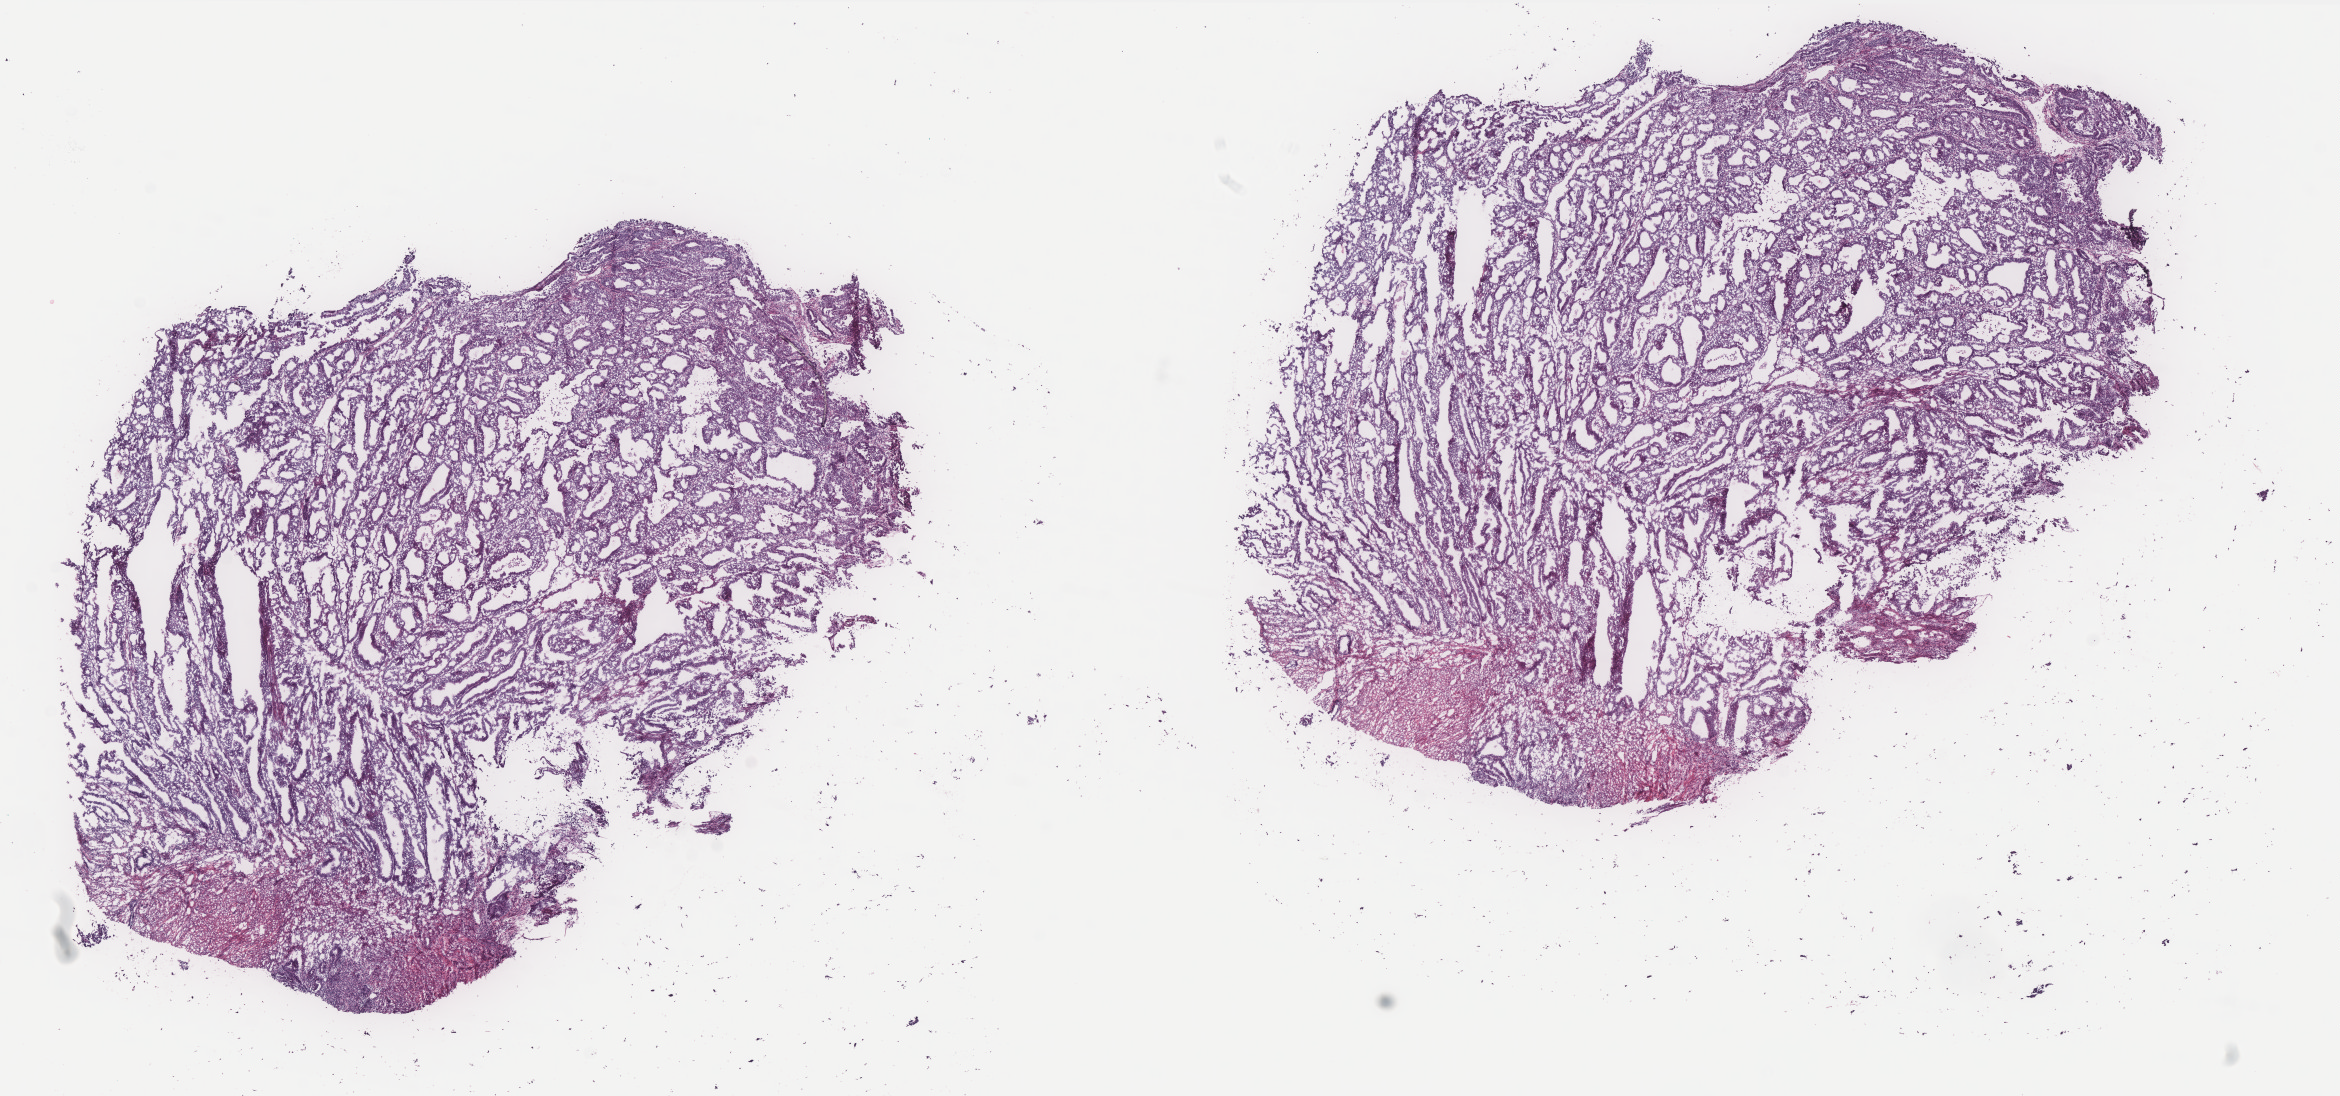
Digitized H&E tissue section (whole slide) — a low-resolution overview of the entire scanned area, about 18.8 x 8.8 mm (from a 40x scan). Frozen section. Primary tumour sample from the uterus. Patient: female, age at initial diagnosis 76 years. Histologic grade: G1 (well differentiated). Slide review estimates, as recorded: tumour cells 90%, tumour nuclei 80%, normal cells 0%, stromal cells 10%, necrosis 0%. Inflammatory infiltration, as recorded: lymphocyte infiltration 0%, monocyte infiltration 0%, neutrophil infiltration 0%.
Histologic diagnosis: Endometrioid adenocarcinoma, NOS (endometrium). FIGO stage: IA.